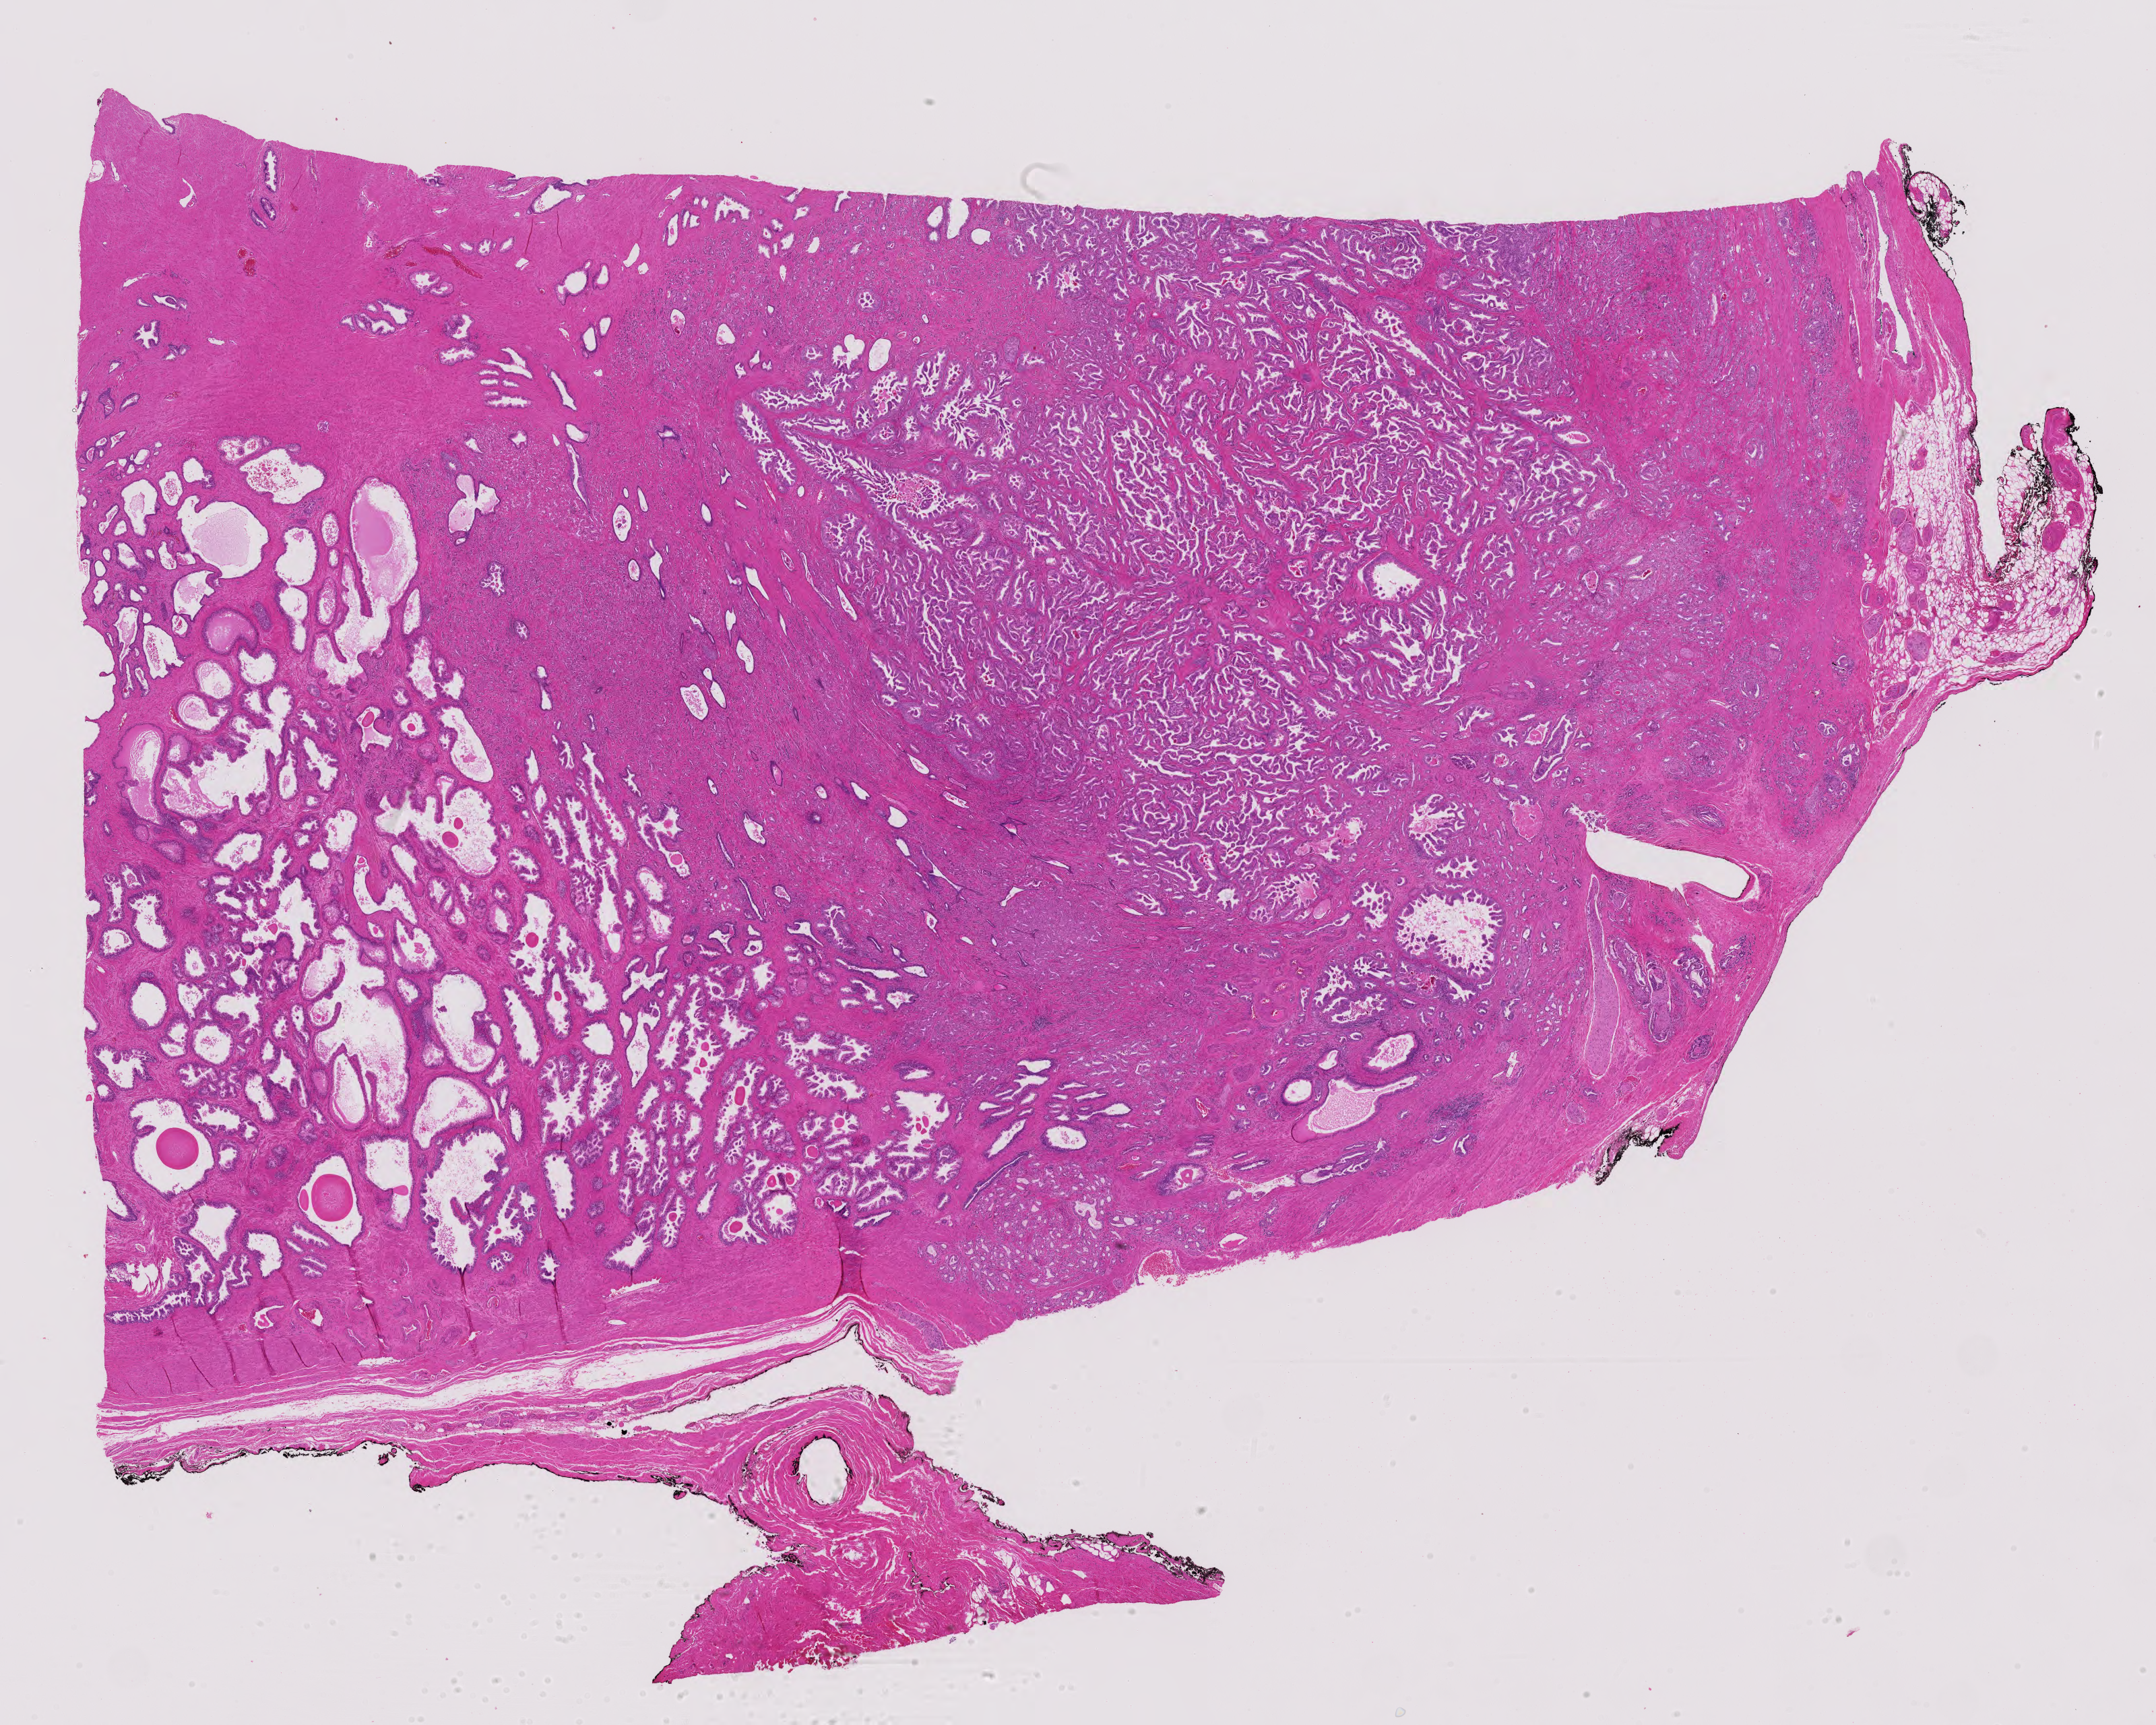
Digitized Hematoxylin and eosin (H&E) stained tissue section (whole slide) — a low-resolution overview of the entire scanned area, about 23.2 x 18.6 mm. FFPE section. Primary tumour sample from the prostate. Patient: male, age at initial diagnosis 69 years. Gleason score: 7 (4+3).
Lymph nodes positive (case pathology): 0 of 21 examined. Diagnosis: Adenocarcinoma, NOS.